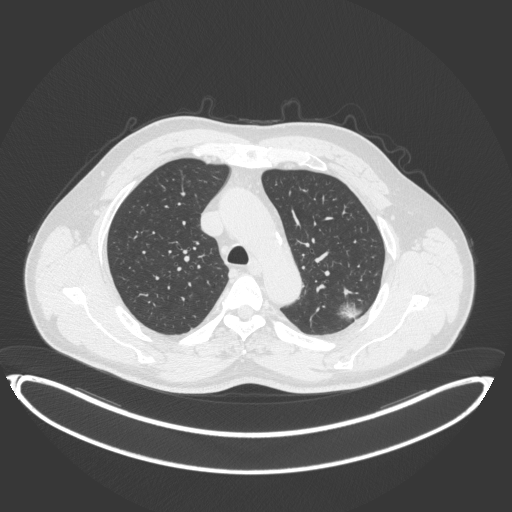
Chest CT, one axial slice; slice 266 of 399 in the series (ordered by position); reconstruction kernel B31f; lung window (W 1500 / L -600 HU); 1 mm slice thickness; 512 × 512 image matrix, field of view 469 × 469 mm. Male patient, age 58 years. Case-level facts recorded for this patient, not image findings: clinical TNM (as recorded): T1c N0 M0; histopathological grade: G1-2.
Annotated regions visible in this slice (rectangle marked by the reading radiologist):
- lung tumour (recorded histology: adenocarcinoma): box from (x=335, y=297) to (x=365, y=324) px